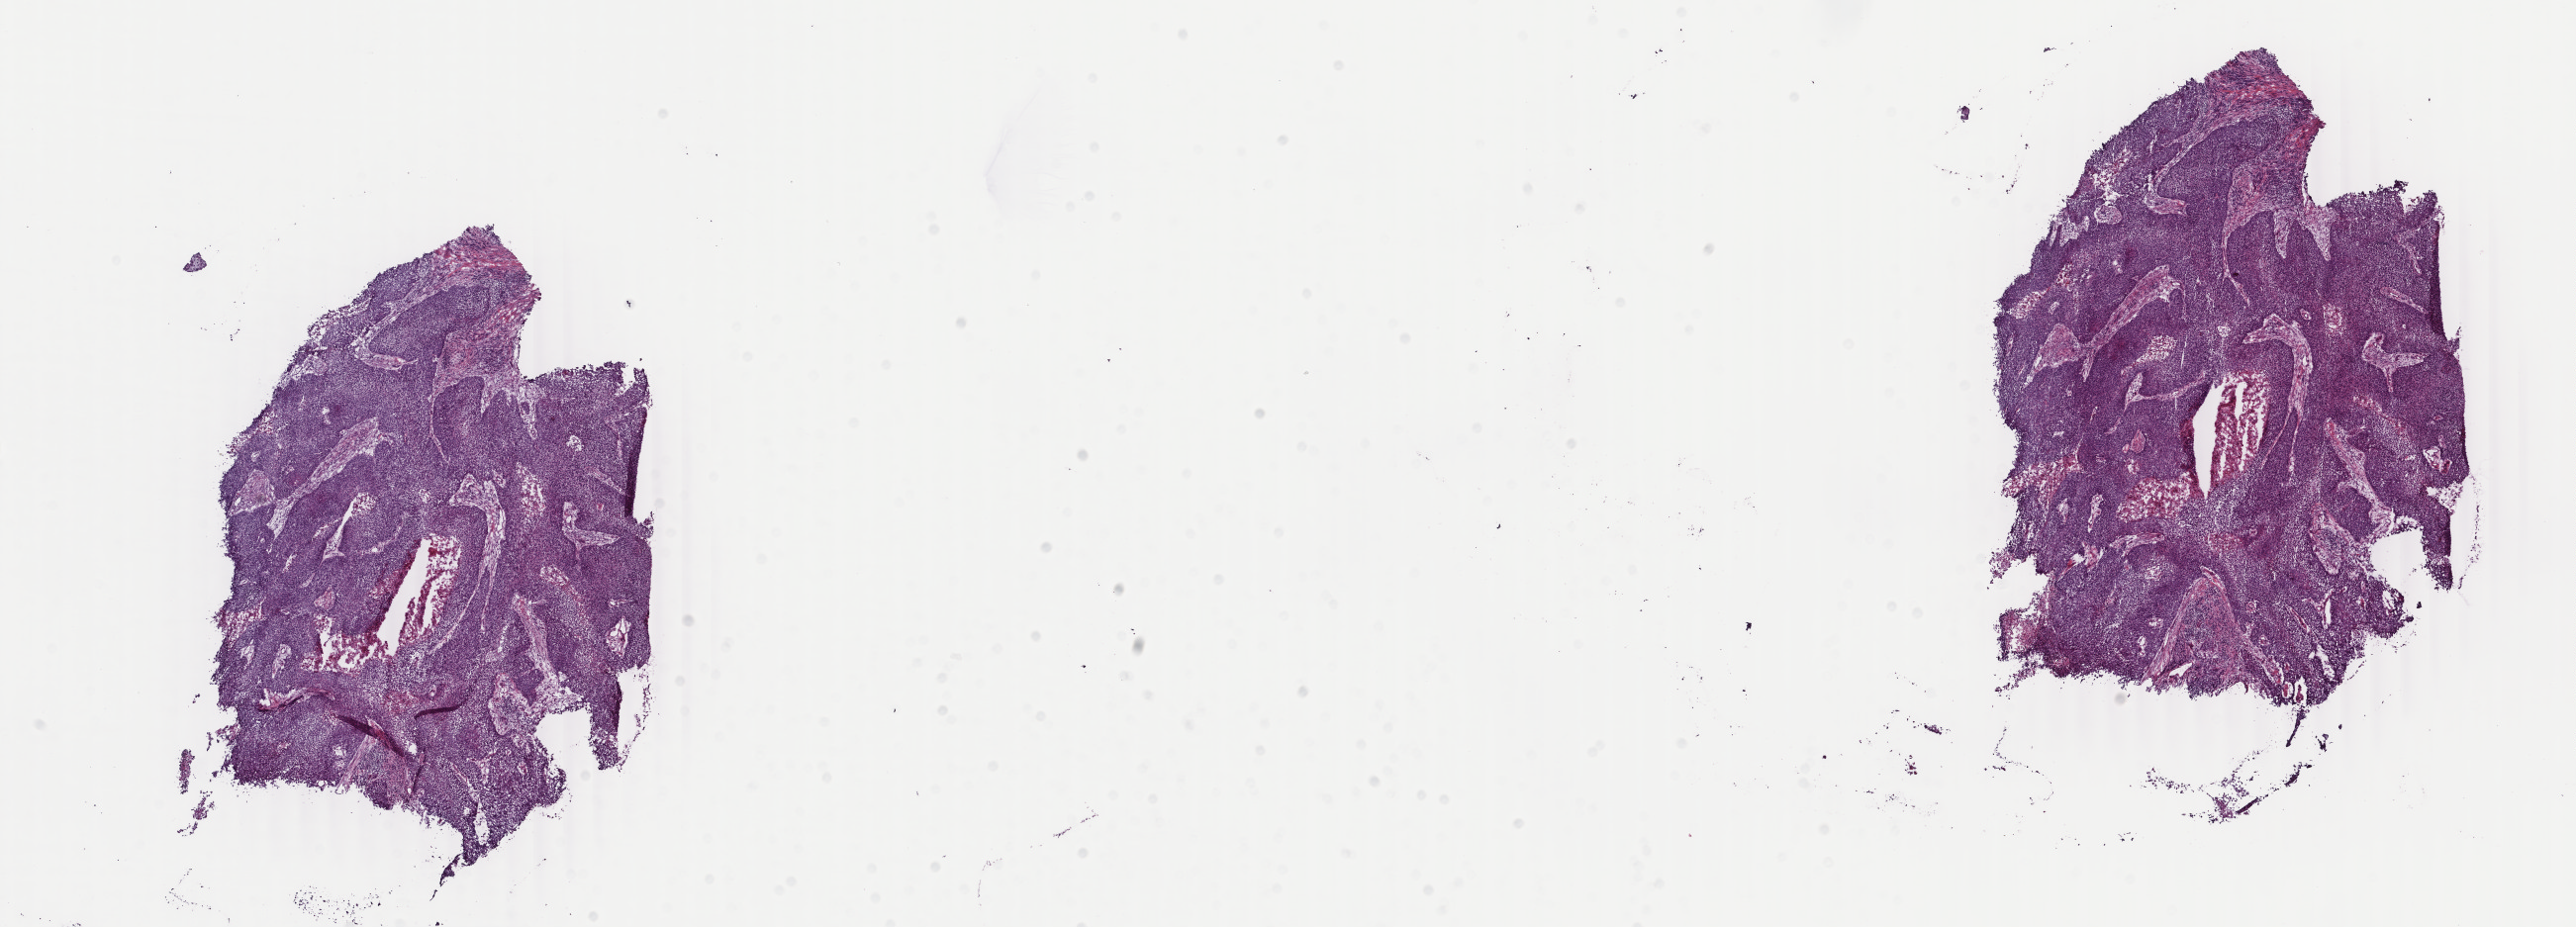
Digitized Hematoxylin and eosin (H&E) stained tissue section (whole slide) — a low-resolution overview of the entire scanned area, about 20.7 x 7.5 mm (from a 40x scan); frozen section from the top of the tissue portion; primary tumour sample from the lung. Male patient; age at initial diagnosis 48 years. Composition of this section per pathologist review: tumour cells 75%, tumour nuclei 75%, normal cells 0%, stromal cells 25%, necrosis 0%. Infiltration values recorded for this section: lymphocyte infiltration 4%, monocyte infiltration 2%, neutrophil infiltration 3%.
Pathologic diagnosis: Squamous cell carcinoma, NOS (lower lobe, lung). TNM: T2b N1 M0. Laterality: right. AJCC pathologic stage: IIB.